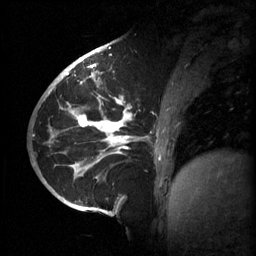
Breast MRI (dynamic contrast-enhanced), one sagittal slice. Slice 23 of 60 in the series (ordered by position). 3 images stored at this slice position (order not interpretable as contrast timing). 1.5 T. TE 4.2 ms, TR 11 ms. 2 mm slice thickness. 256 × 256 image matrix, field of view 220 × 220 mm. Female patient, age 51 years.
Structures marked on this image (semi-automatically segmented with operator editing):
- analysis volume of interest (the breast-tissue region the enhancement analysis was run in; not a lesion): box from (x=63, y=80) to (x=187, y=201) px
- tumour enhancement mask (voxels above the 70 % enhancement threshold inside the analysis volume of interest): (x=68, y=80)–(x=161, y=167)